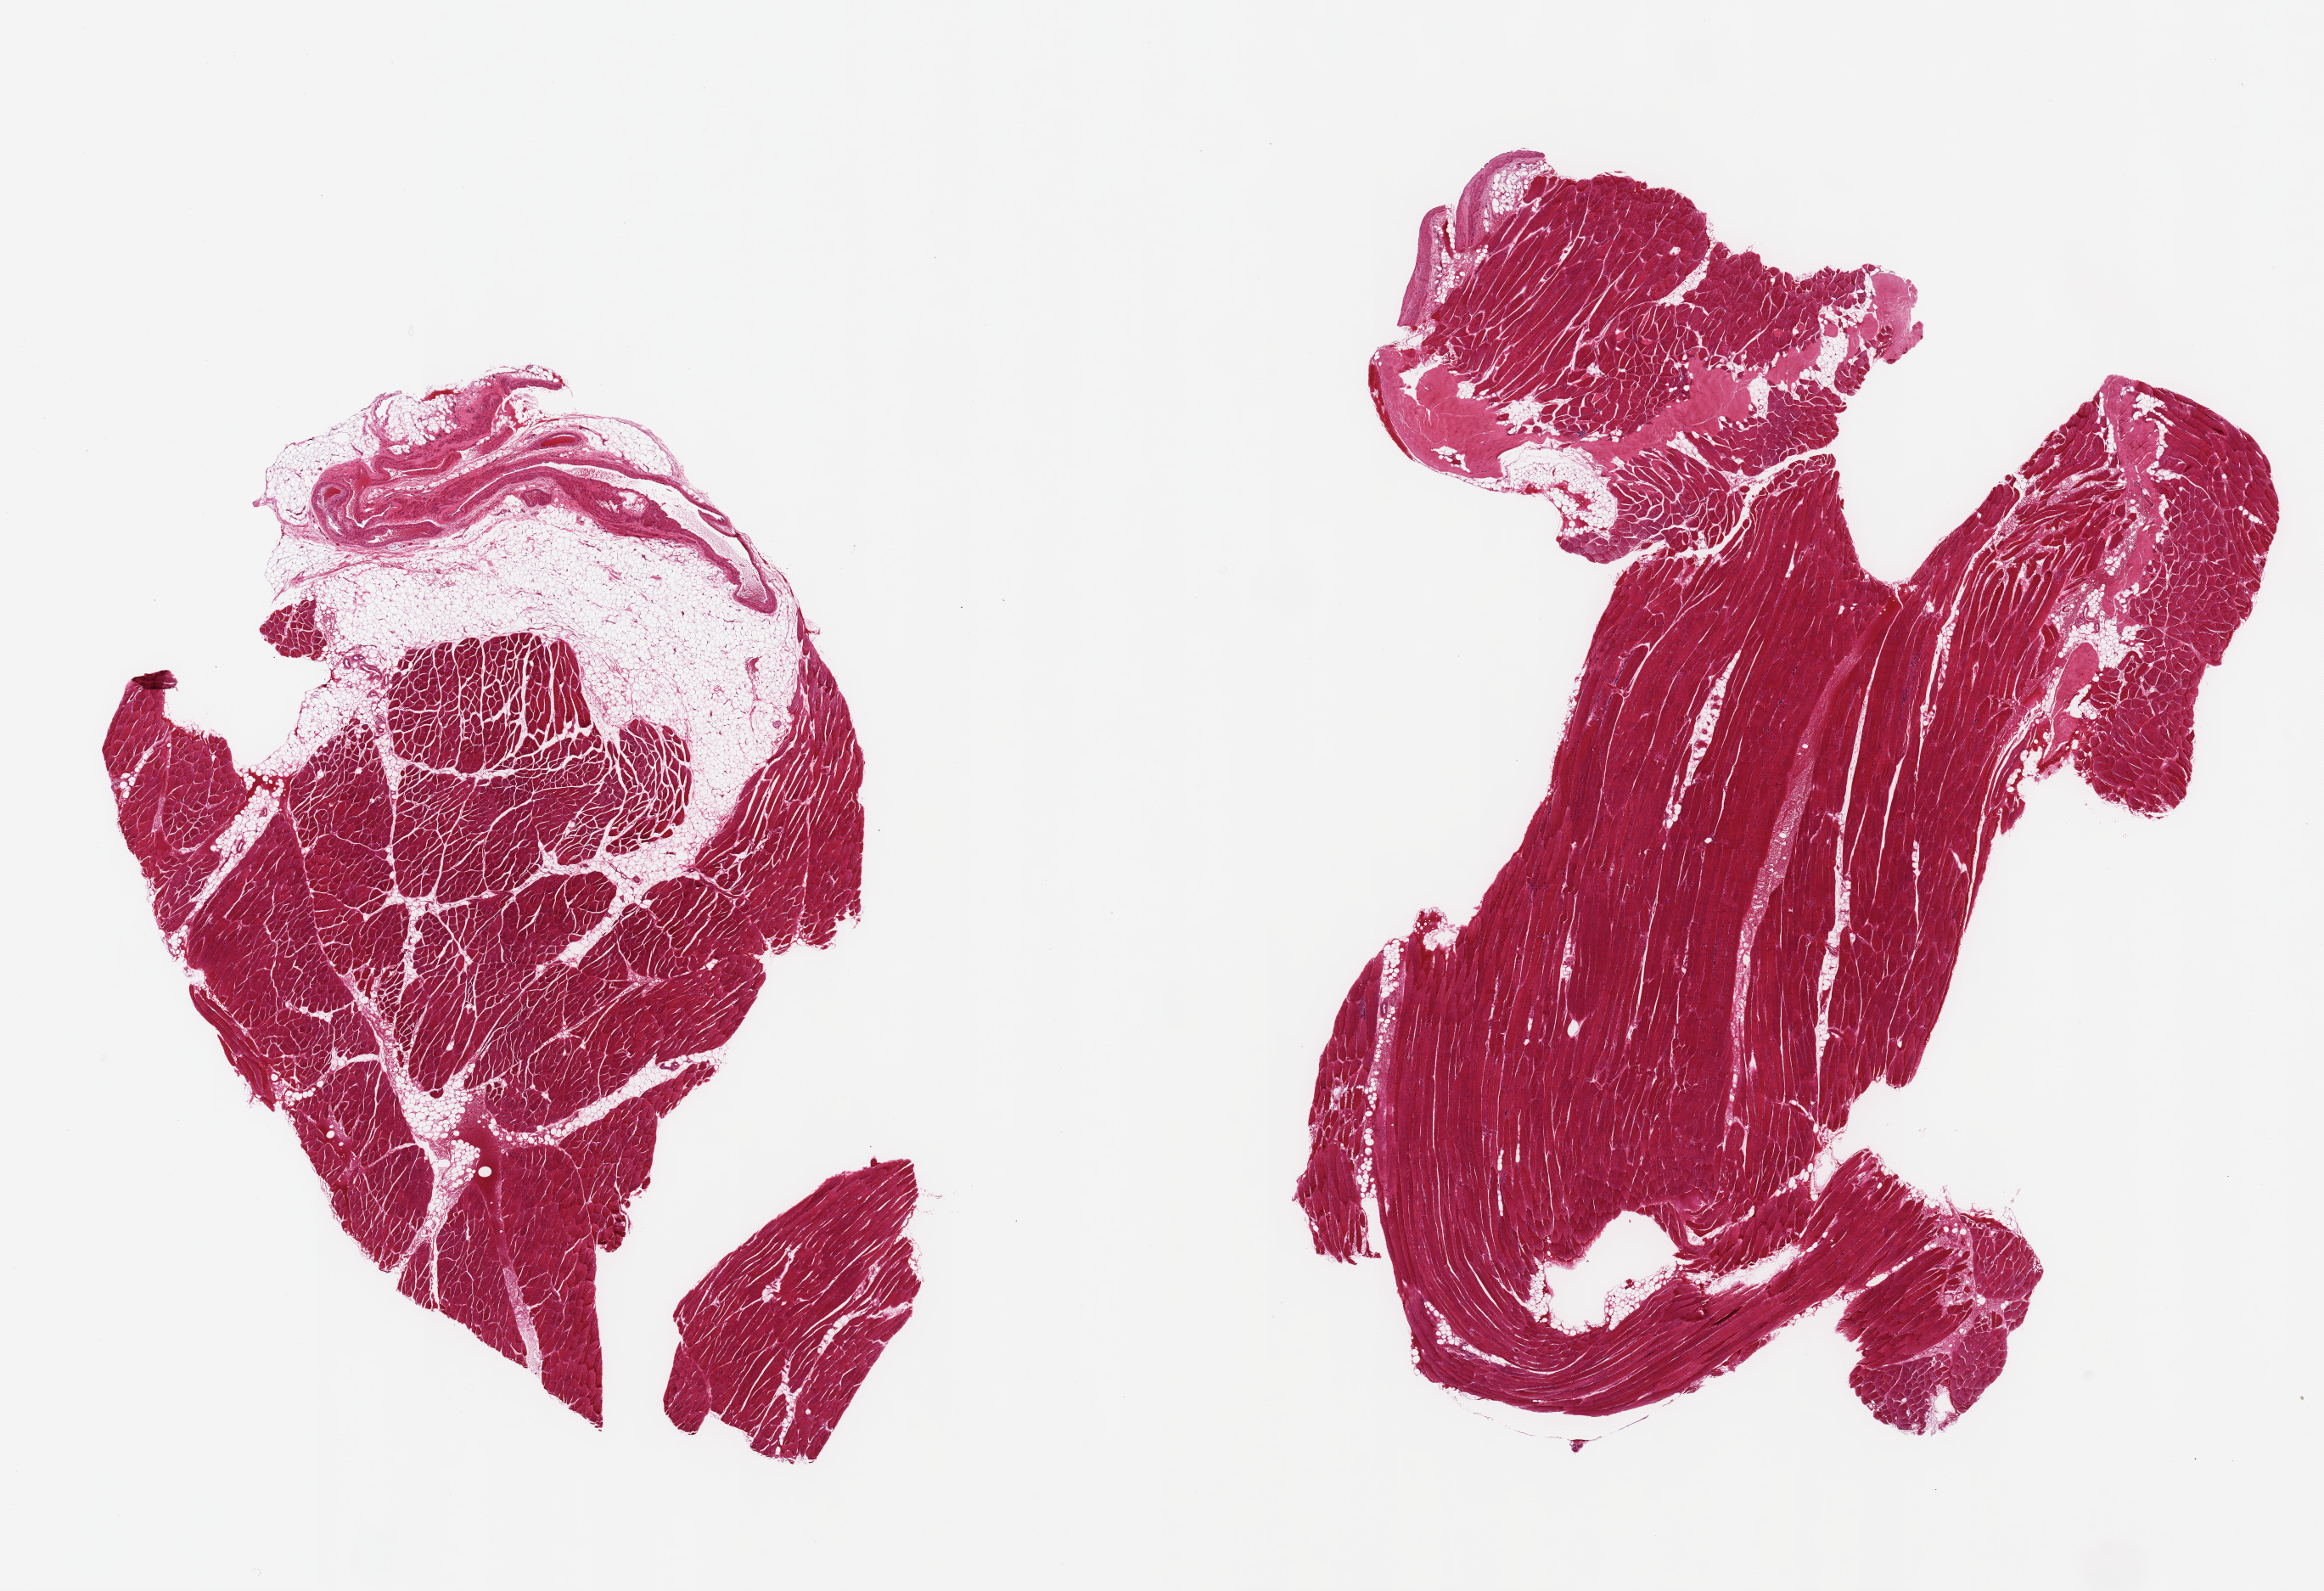
H&E whole-slide image, whole scanned area (about 21.7 x 14.8 mm, slide scanned at 20x) shown as a low-resolution overview. PAXgene-fixed paraffin-embedded (PFPE) section. Section of skeletal muscle (target tissue). Donor tissue sample. Donor sex: female.
* review note (as recorded): 2 pieces; 1 has 20% fat & large vessels; other has <5% fat